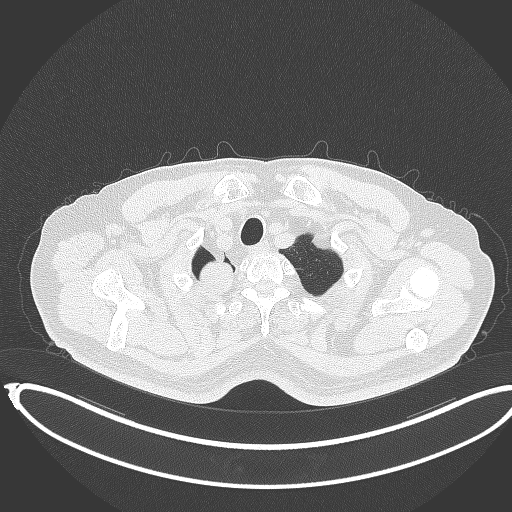
Chest CT, one axial slice. Slice 341 of 403 in the series (ordered by position). Lung window (W 1500 / L -600 HU). 1 mm slice thickness. 512 × 512 image matrix, field of view 436 × 436 mm. Male patient, age 68 years. From the clinical record (not read from this slice): clinical TNM (as recorded): T2a N0 M0.
Outlined on this slice (rectangle marked by the reading radiologist):
- lung tumour (recorded histology: adenocarcinoma): bounding box <195,257,238,298> (left, top, right, bottom; pixels)